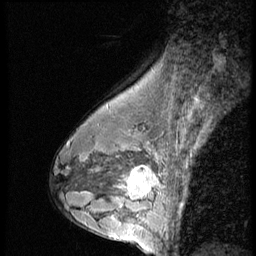
Breast MRI (dynamic contrast-enhanced), one sagittal slice. Position 37 of 56 along the scan axis. 3 images stored at this slice position (order not interpretable as contrast timing). 1.5 T. TE 4.2 ms, TR 9 ms. 2.5 mm slice thickness. 256 × 256 image matrix. Female patient, age 43 years. Case-level facts recorded for this patient, not image findings: setting: breast cancer imaged before/during neoadjuvant chemotherapy; receptor status: HR-positive, HER2-negative.
Structures marked on this image (semi-automatically segmented with operator editing):
- analysis volume of interest (the breast-tissue region the enhancement analysis was run in; not a lesion): bounding box (x1, y1, x2, y2) in pixels: (120, 160, 163, 207)
- tumour enhancement mask (voxels above the 140 % enhancement threshold inside the analysis volume of interest): (128, 166, 159, 199)